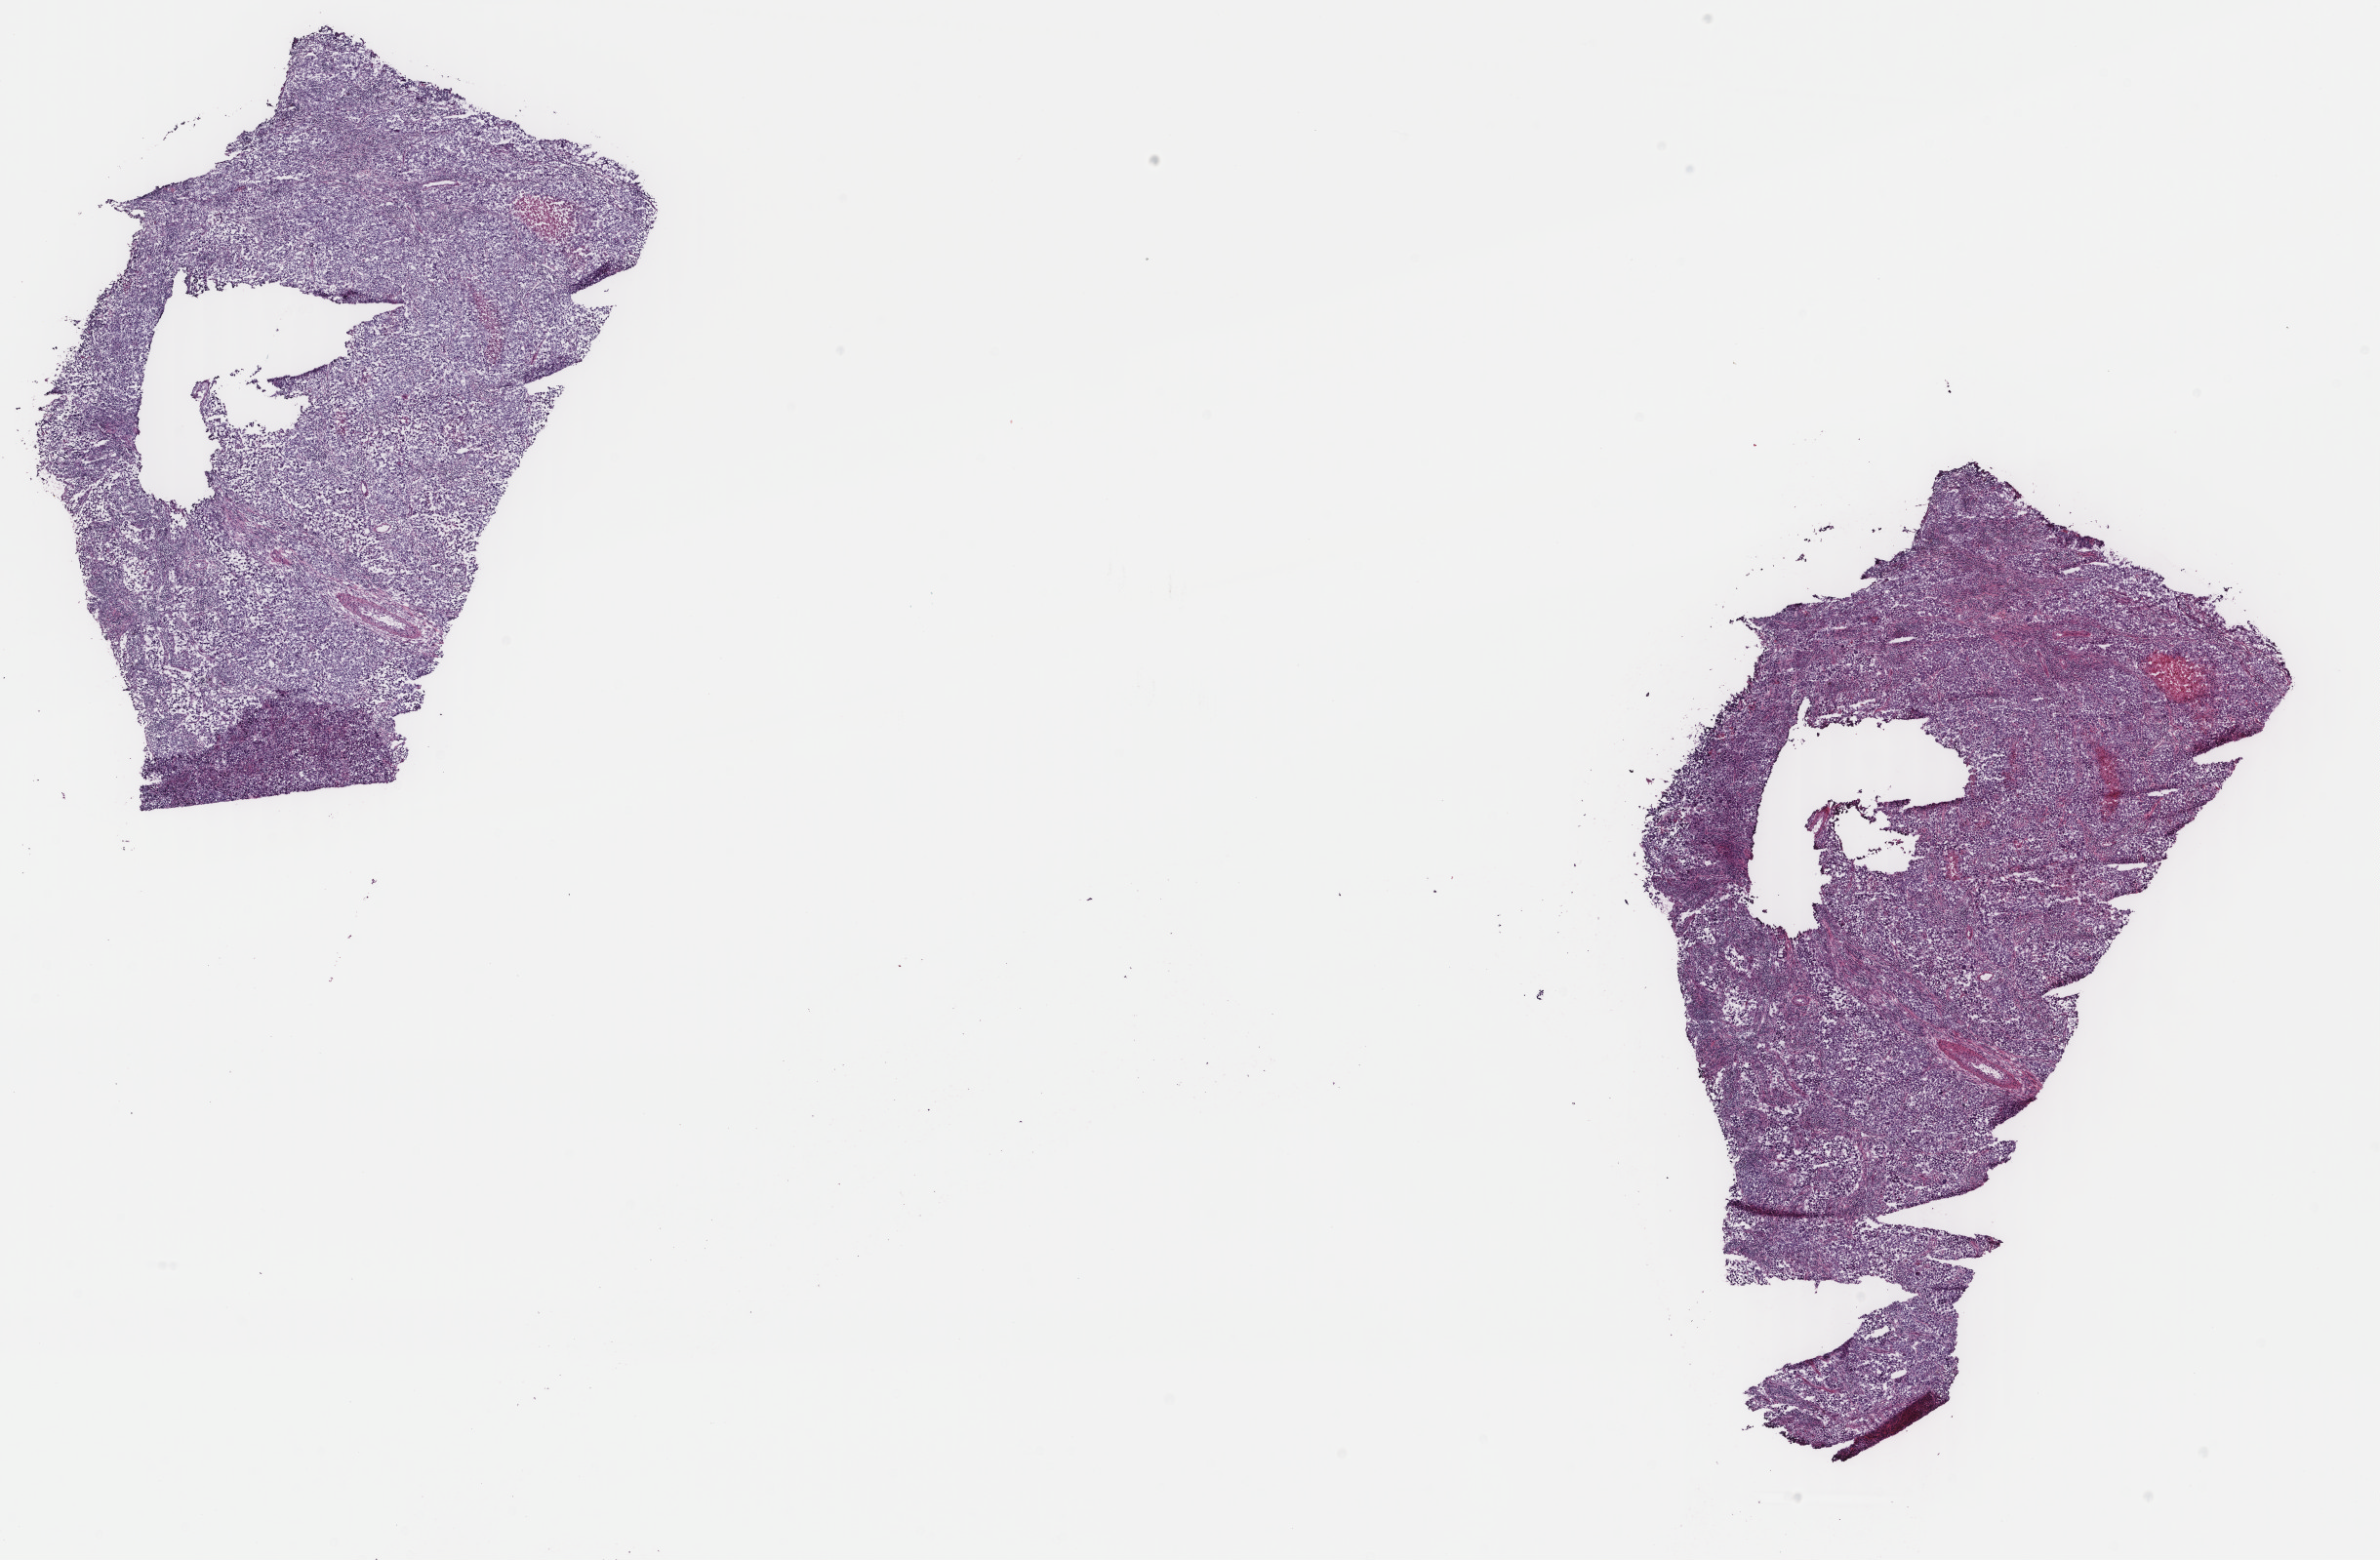
H&E-stained whole-slide image, whole scanned area (about 19.4 x 12.7 mm) shown as a low-resolution overview, frozen section from the top of the tissue portion, metastatic tumour sample. Female patient; age at initial diagnosis 43 years. Slide review estimates, as recorded: tumour cells 80%, tumour nuclei 80%, normal cells 1%, stromal cells 16%, necrosis 3%. Infiltration values recorded for this section: lymphocyte infiltration 3%, monocyte infiltration 2%, neutrophil infiltration 0%.
- this section: metastatic tumour tissue
- patient diagnosis: Malignant melanoma, NOS